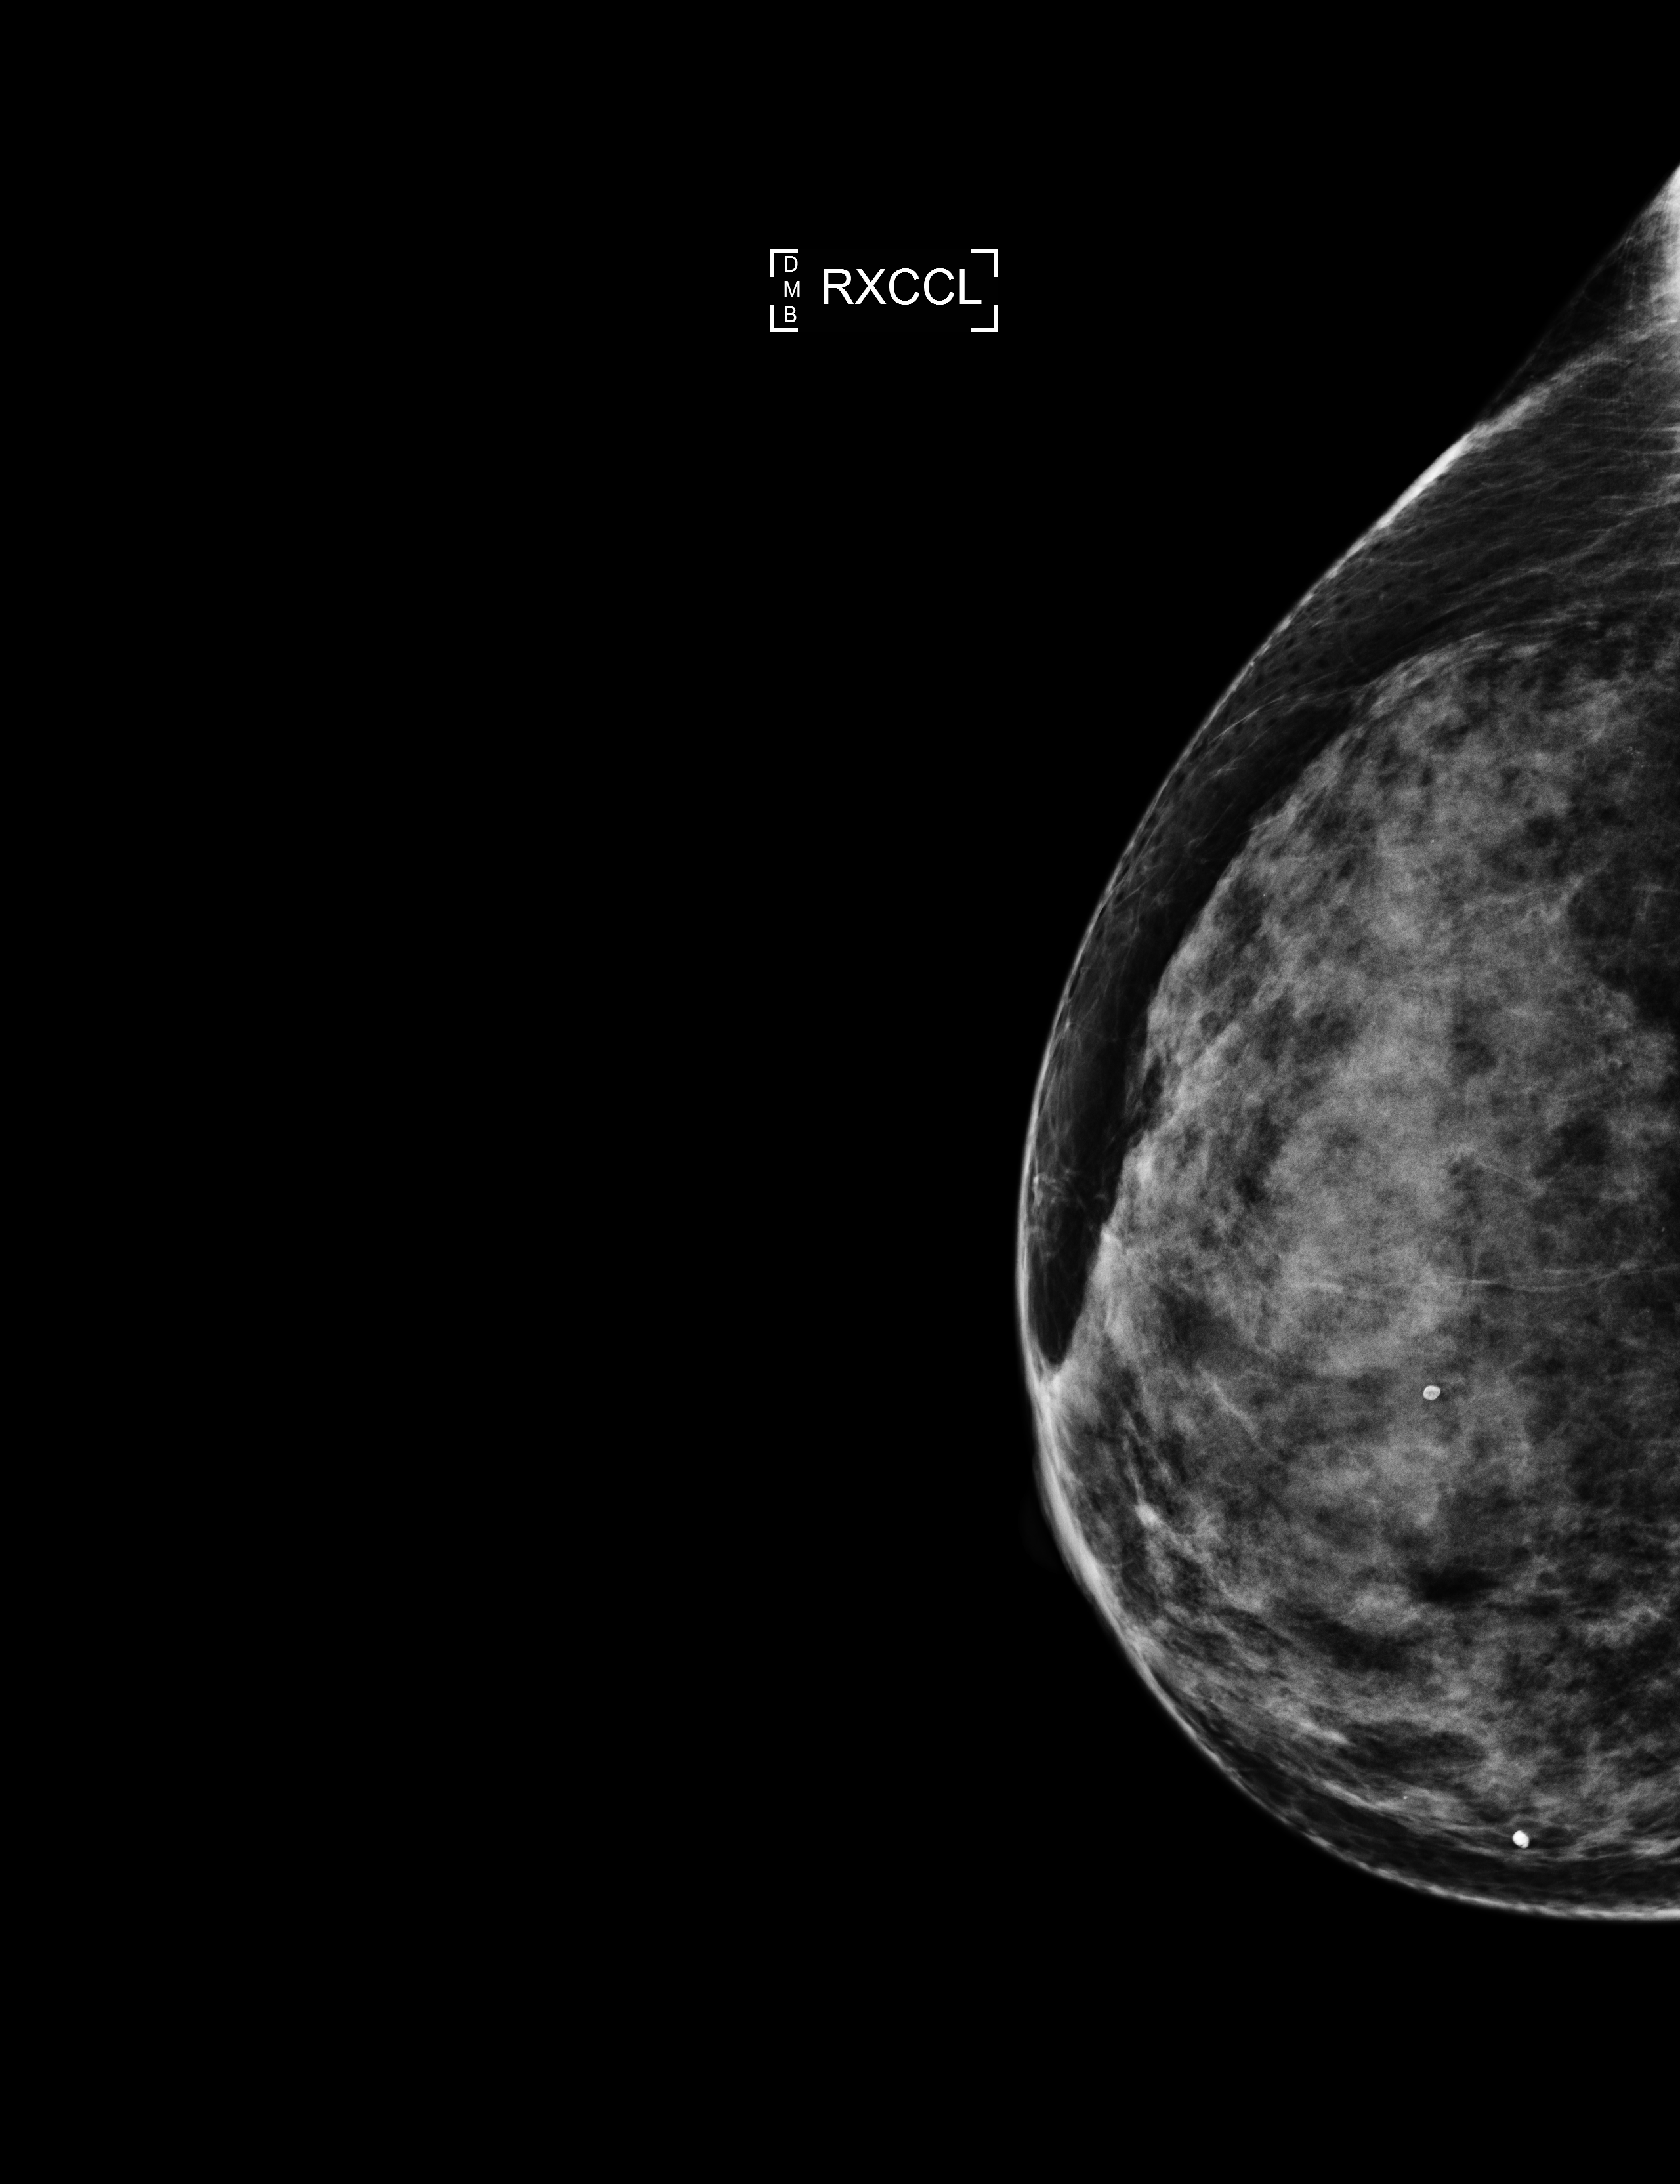
Full-field digital mammogram (FFDM); right breast; laterally exaggerated craniocaudal (XCCL) view; screening examination; system: Selenia Dimensions. Patient: female, 62 years.
Breast density at the screening exam (both breasts): extremely dense (BI-RADS density category d). Final BI-RADS category for the screening round (tomosynthesis exam, both breasts): category 1. Recall: no recall after this screen.